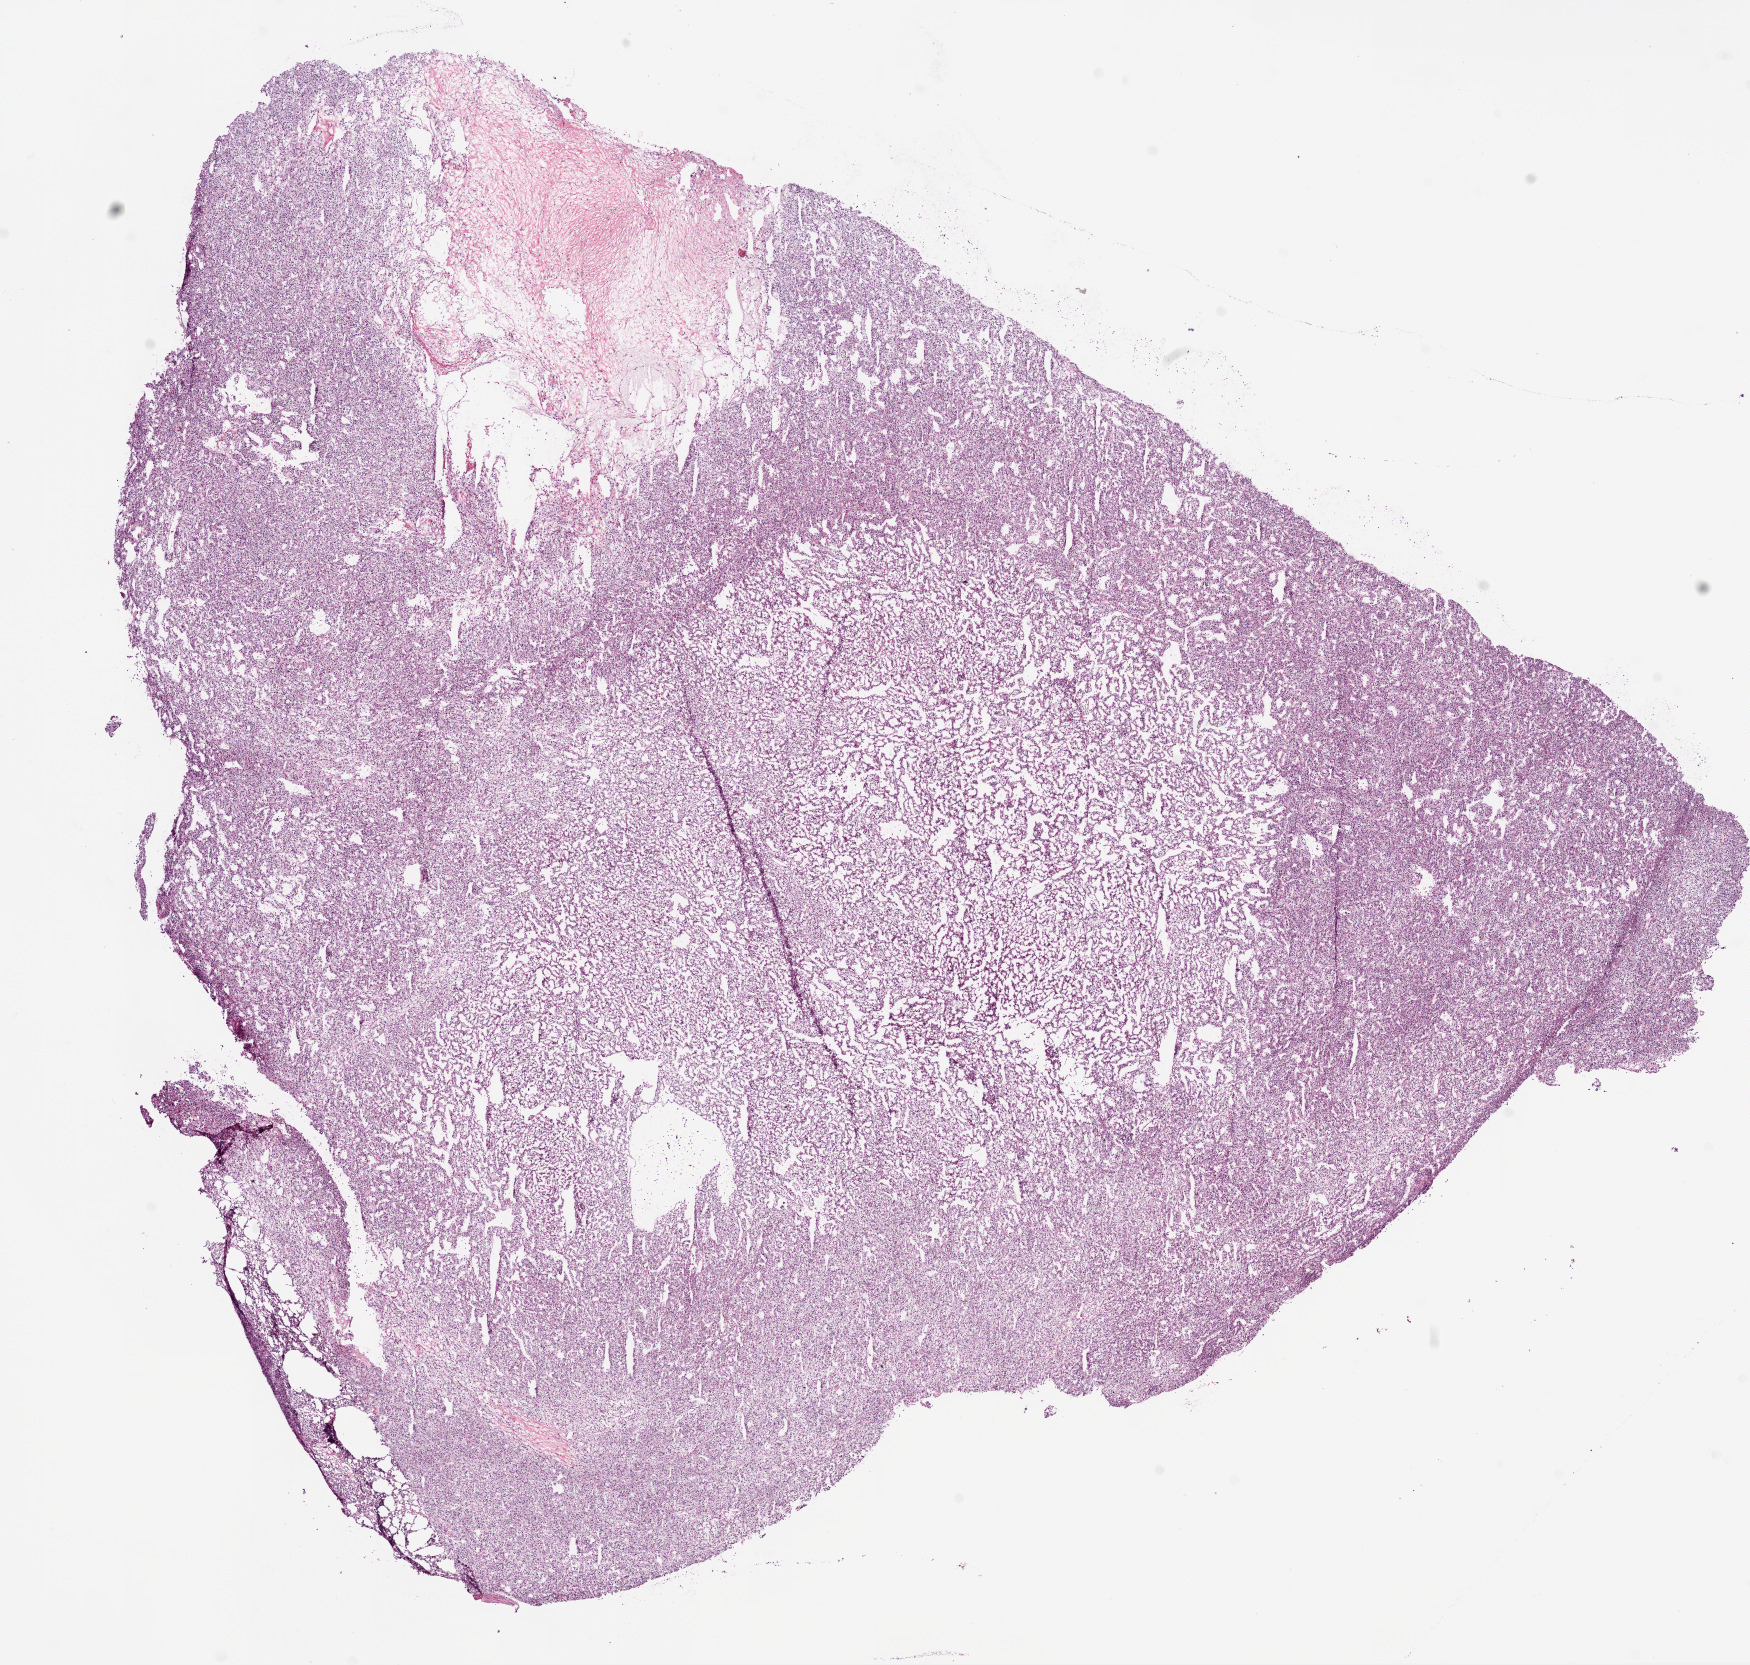
Digitized H&E tissue section (whole slide) — shown as a low-resolution overview of the whole scanned area (about 14.0 x 13.4 mm, from a 20x scan); frozen section from the bottom of the tissue portion; primary tumour sample from the kidney. Male patient; age at initial diagnosis 70 years. Histologic grade: G2 (moderately differentiated). Pathologist review of this section (percent, as recorded): tumour cells 85%, tumour nuclei 90%, normal cells 0%, stromal cells 15%, necrosis 0%.
- diagnosis: Clear cell adenocarcinoma, NOS
- AJCC pathologic stage: IV